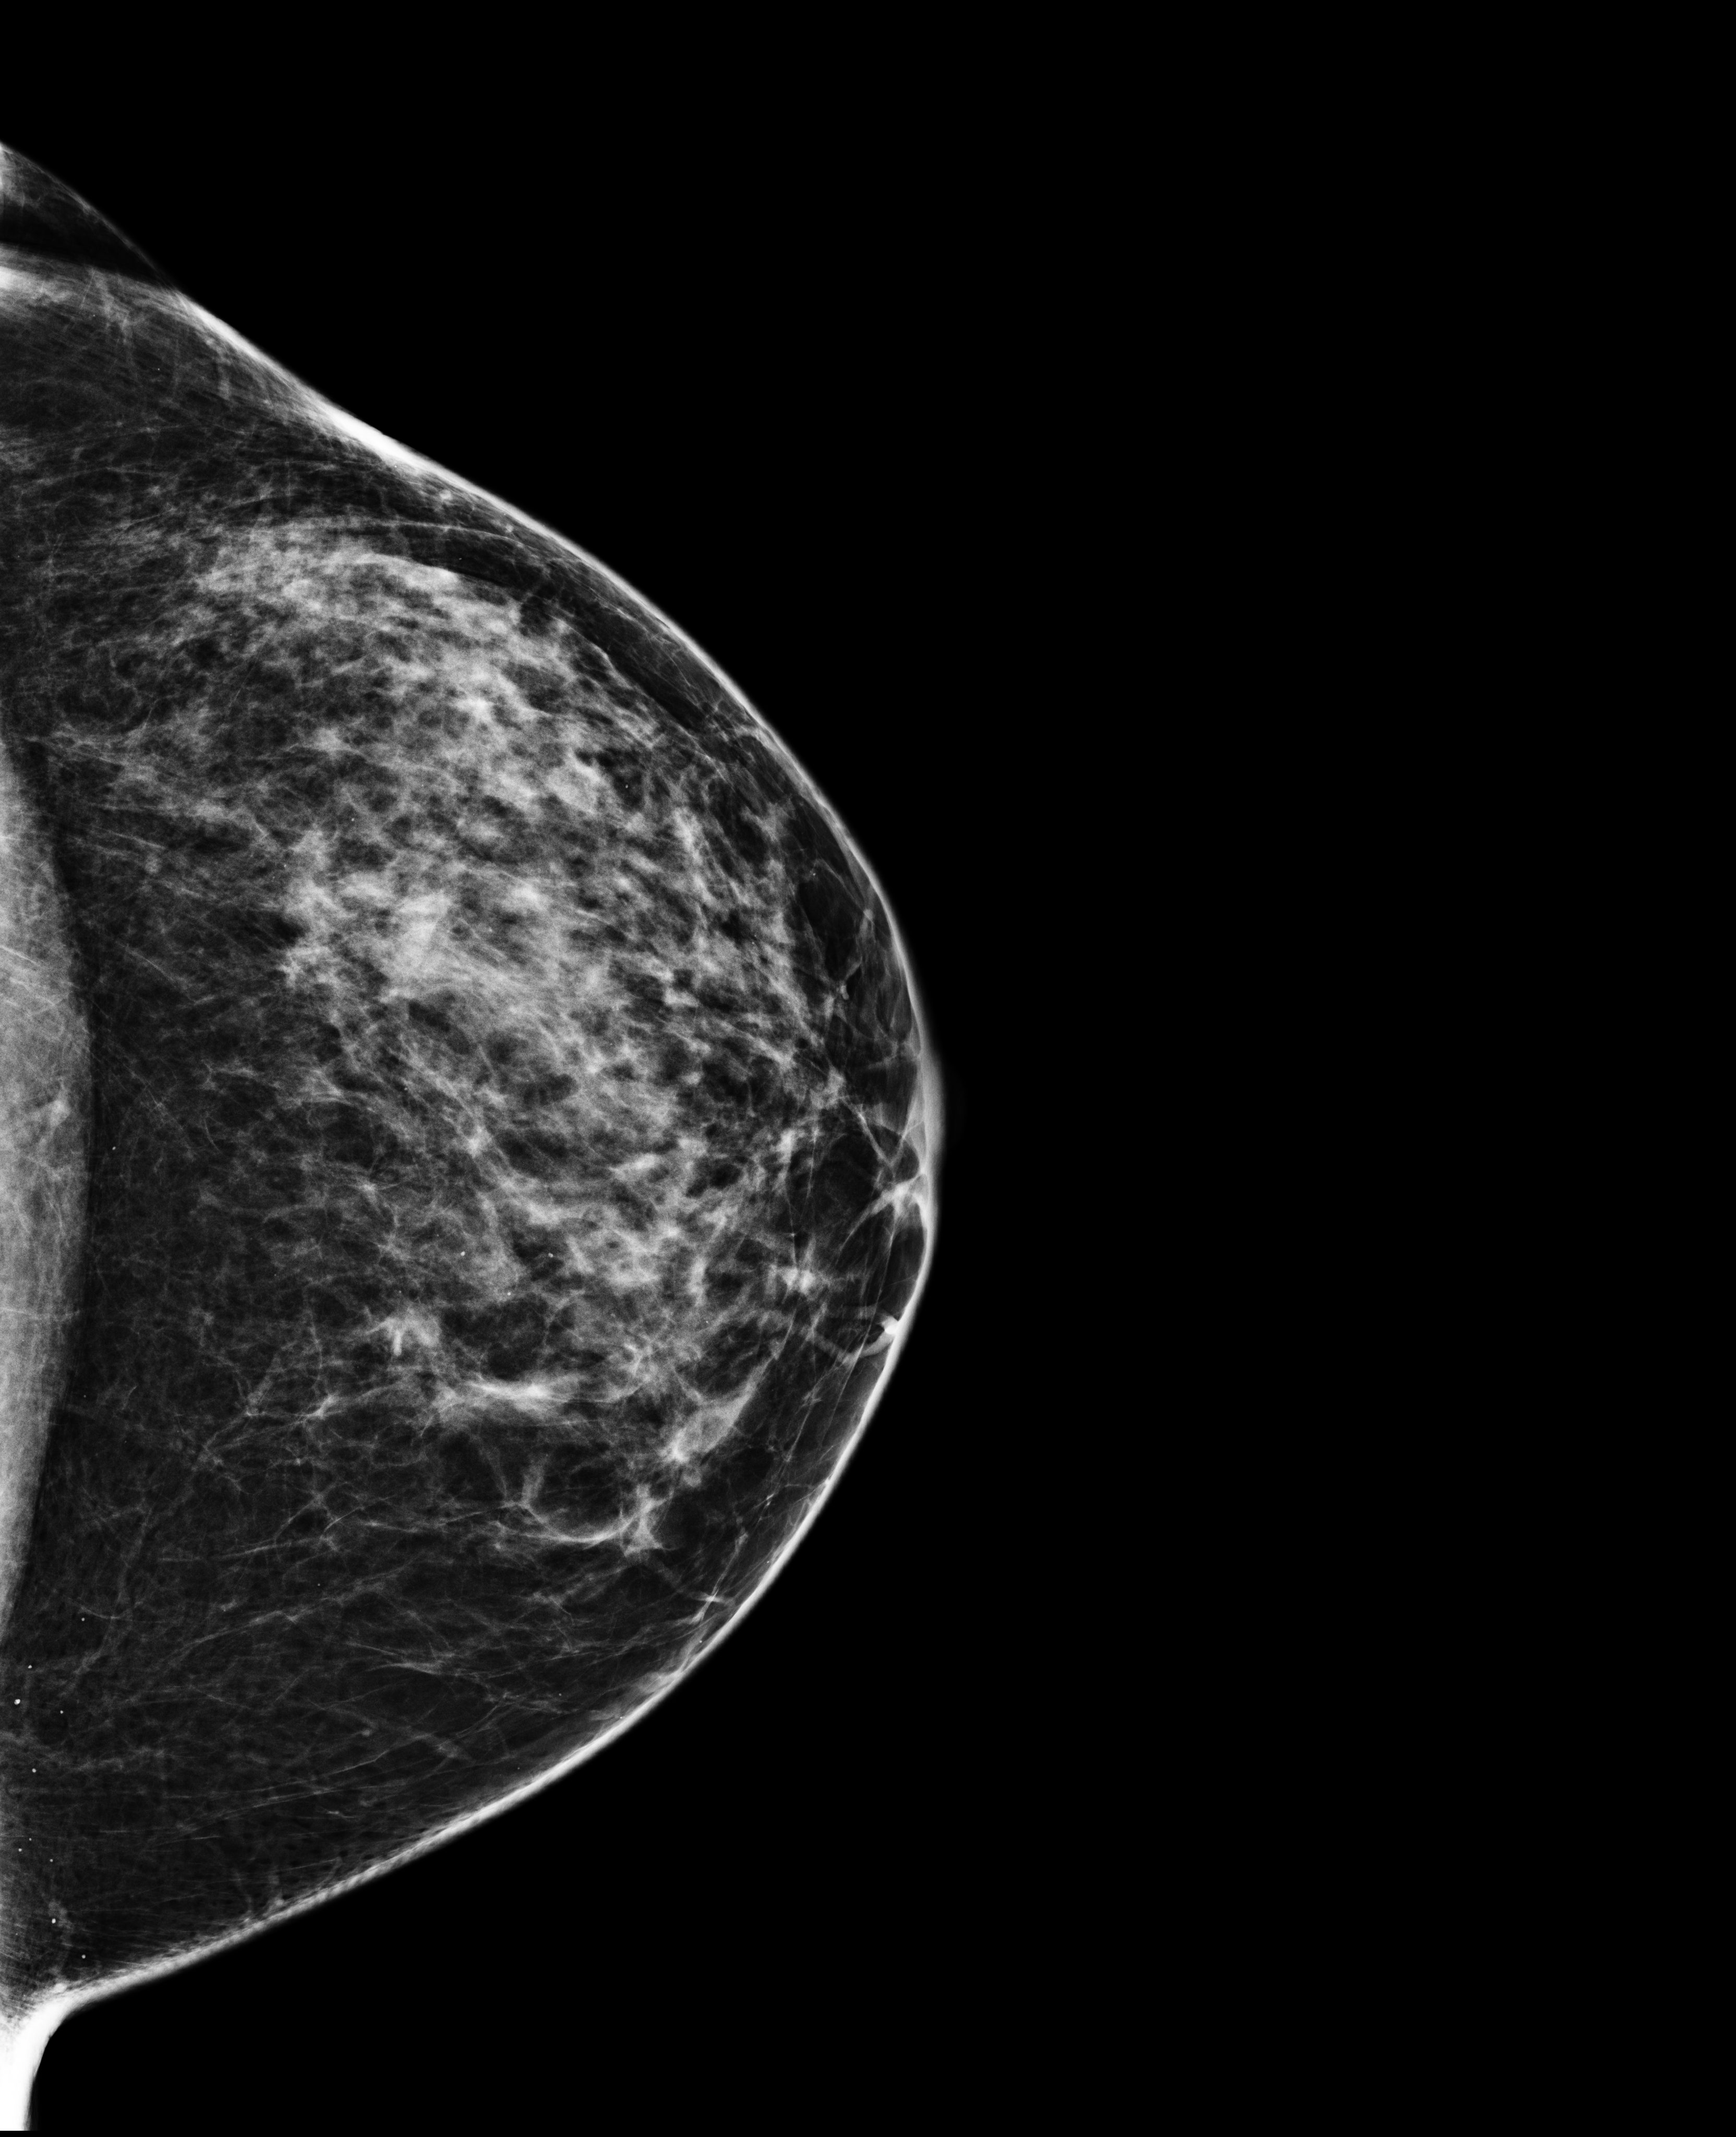
Screening examination. Patient aged 49 years (female).
Image type: full-field digital mammogram. Breast: left. Projection: CC view.